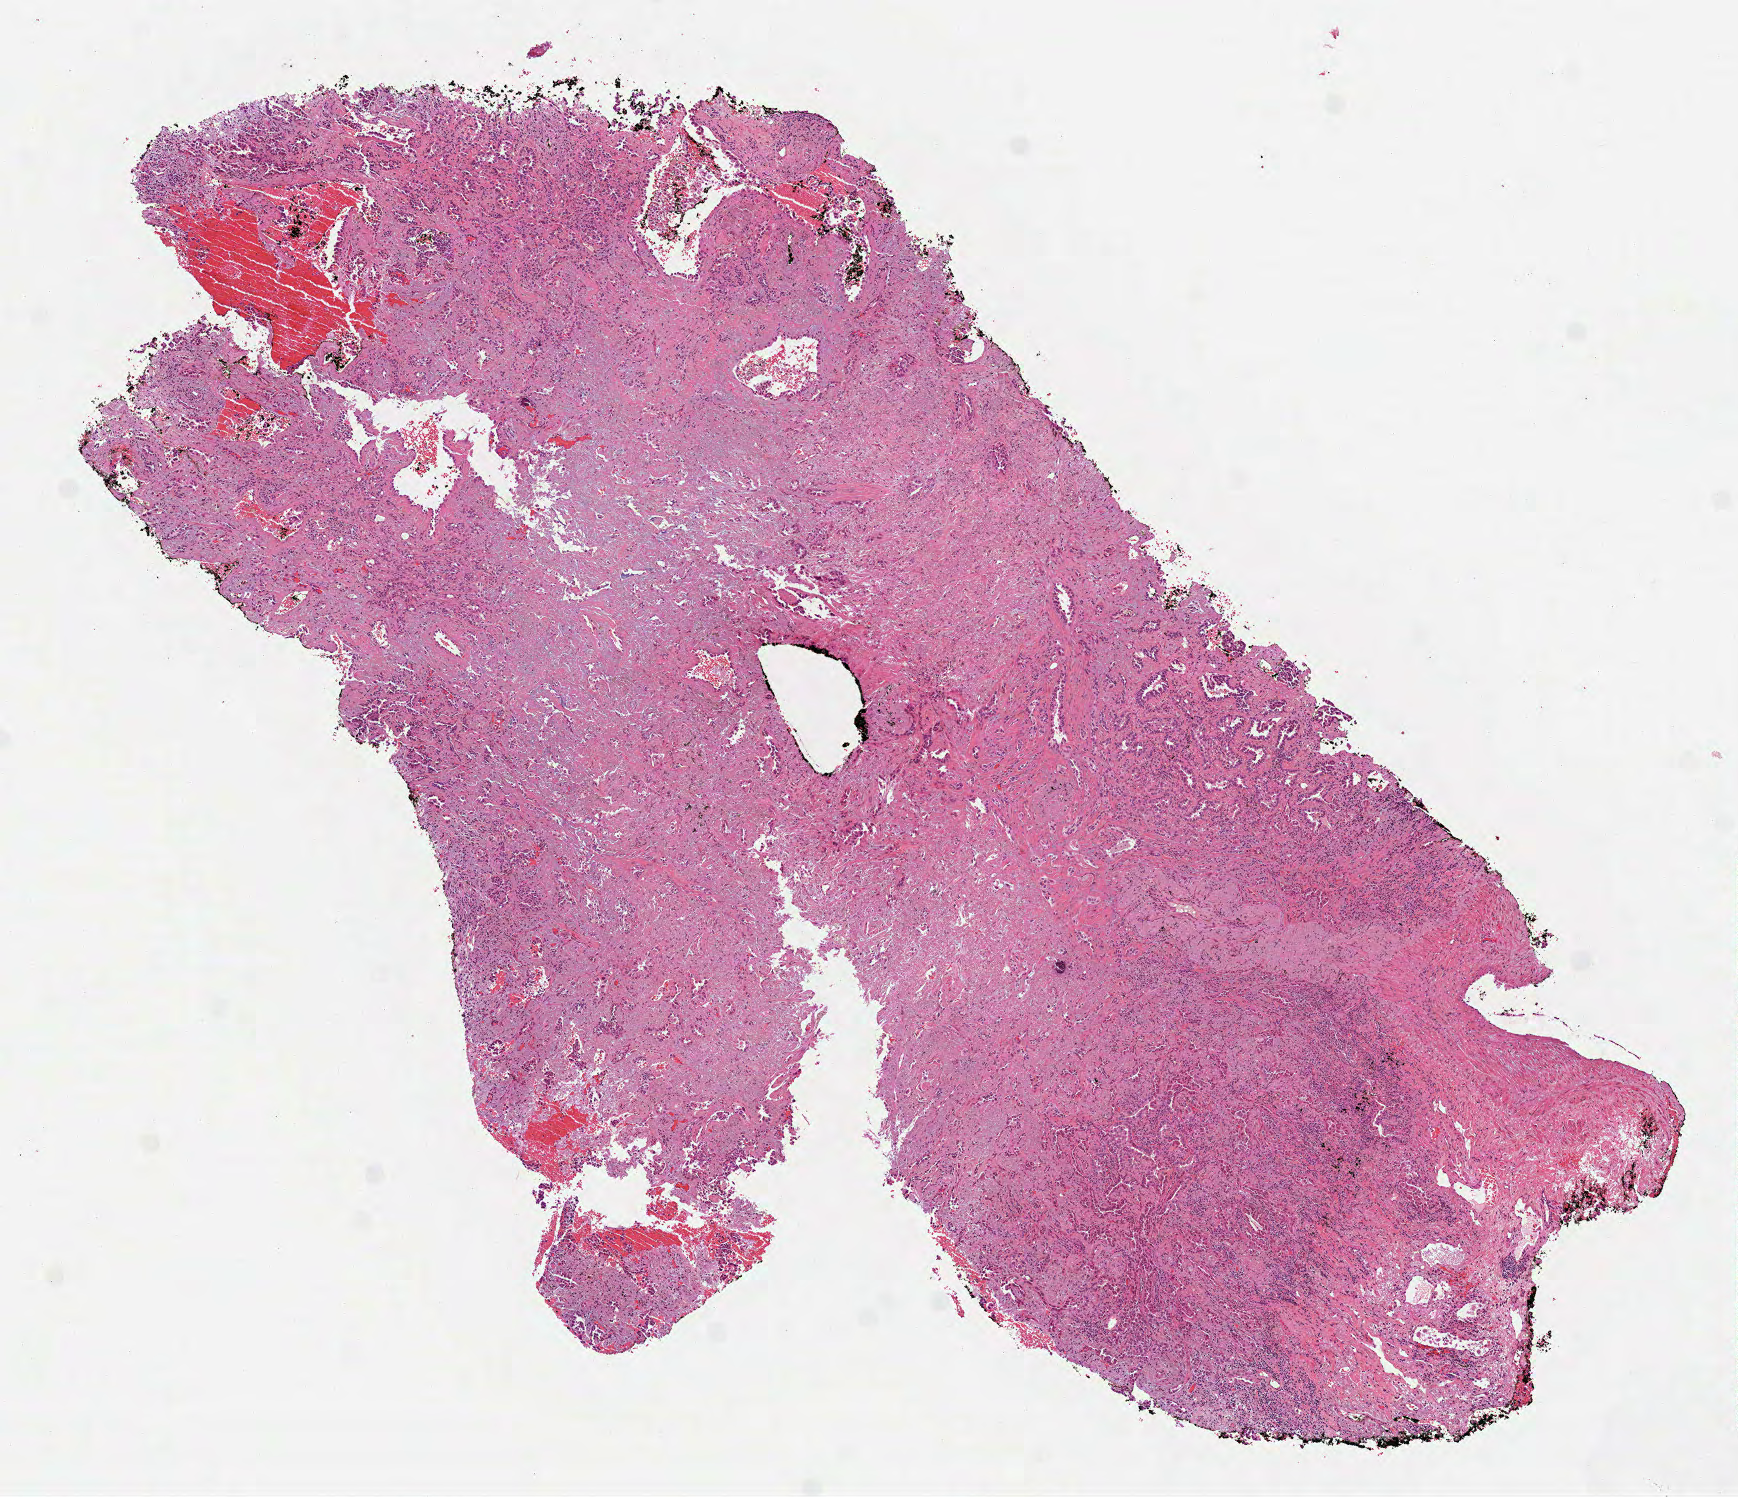
Digitized Hematoxylin and eosin (H&E) stained tissue section (whole slide), shown as a low-resolution overview of the whole scanned area (about 7.0 x 6.0 mm), formalin-fixed paraffin-embedded (FFPE) diagnostic section, lung, primary tumour sample. Male patient; age at initial diagnosis 71 years.
Laterality: right. AJCC pathologic stage: IA (7th edition). Pathologic diagnosis: Adenocarcinoma, NOS (upper lobe, lung).